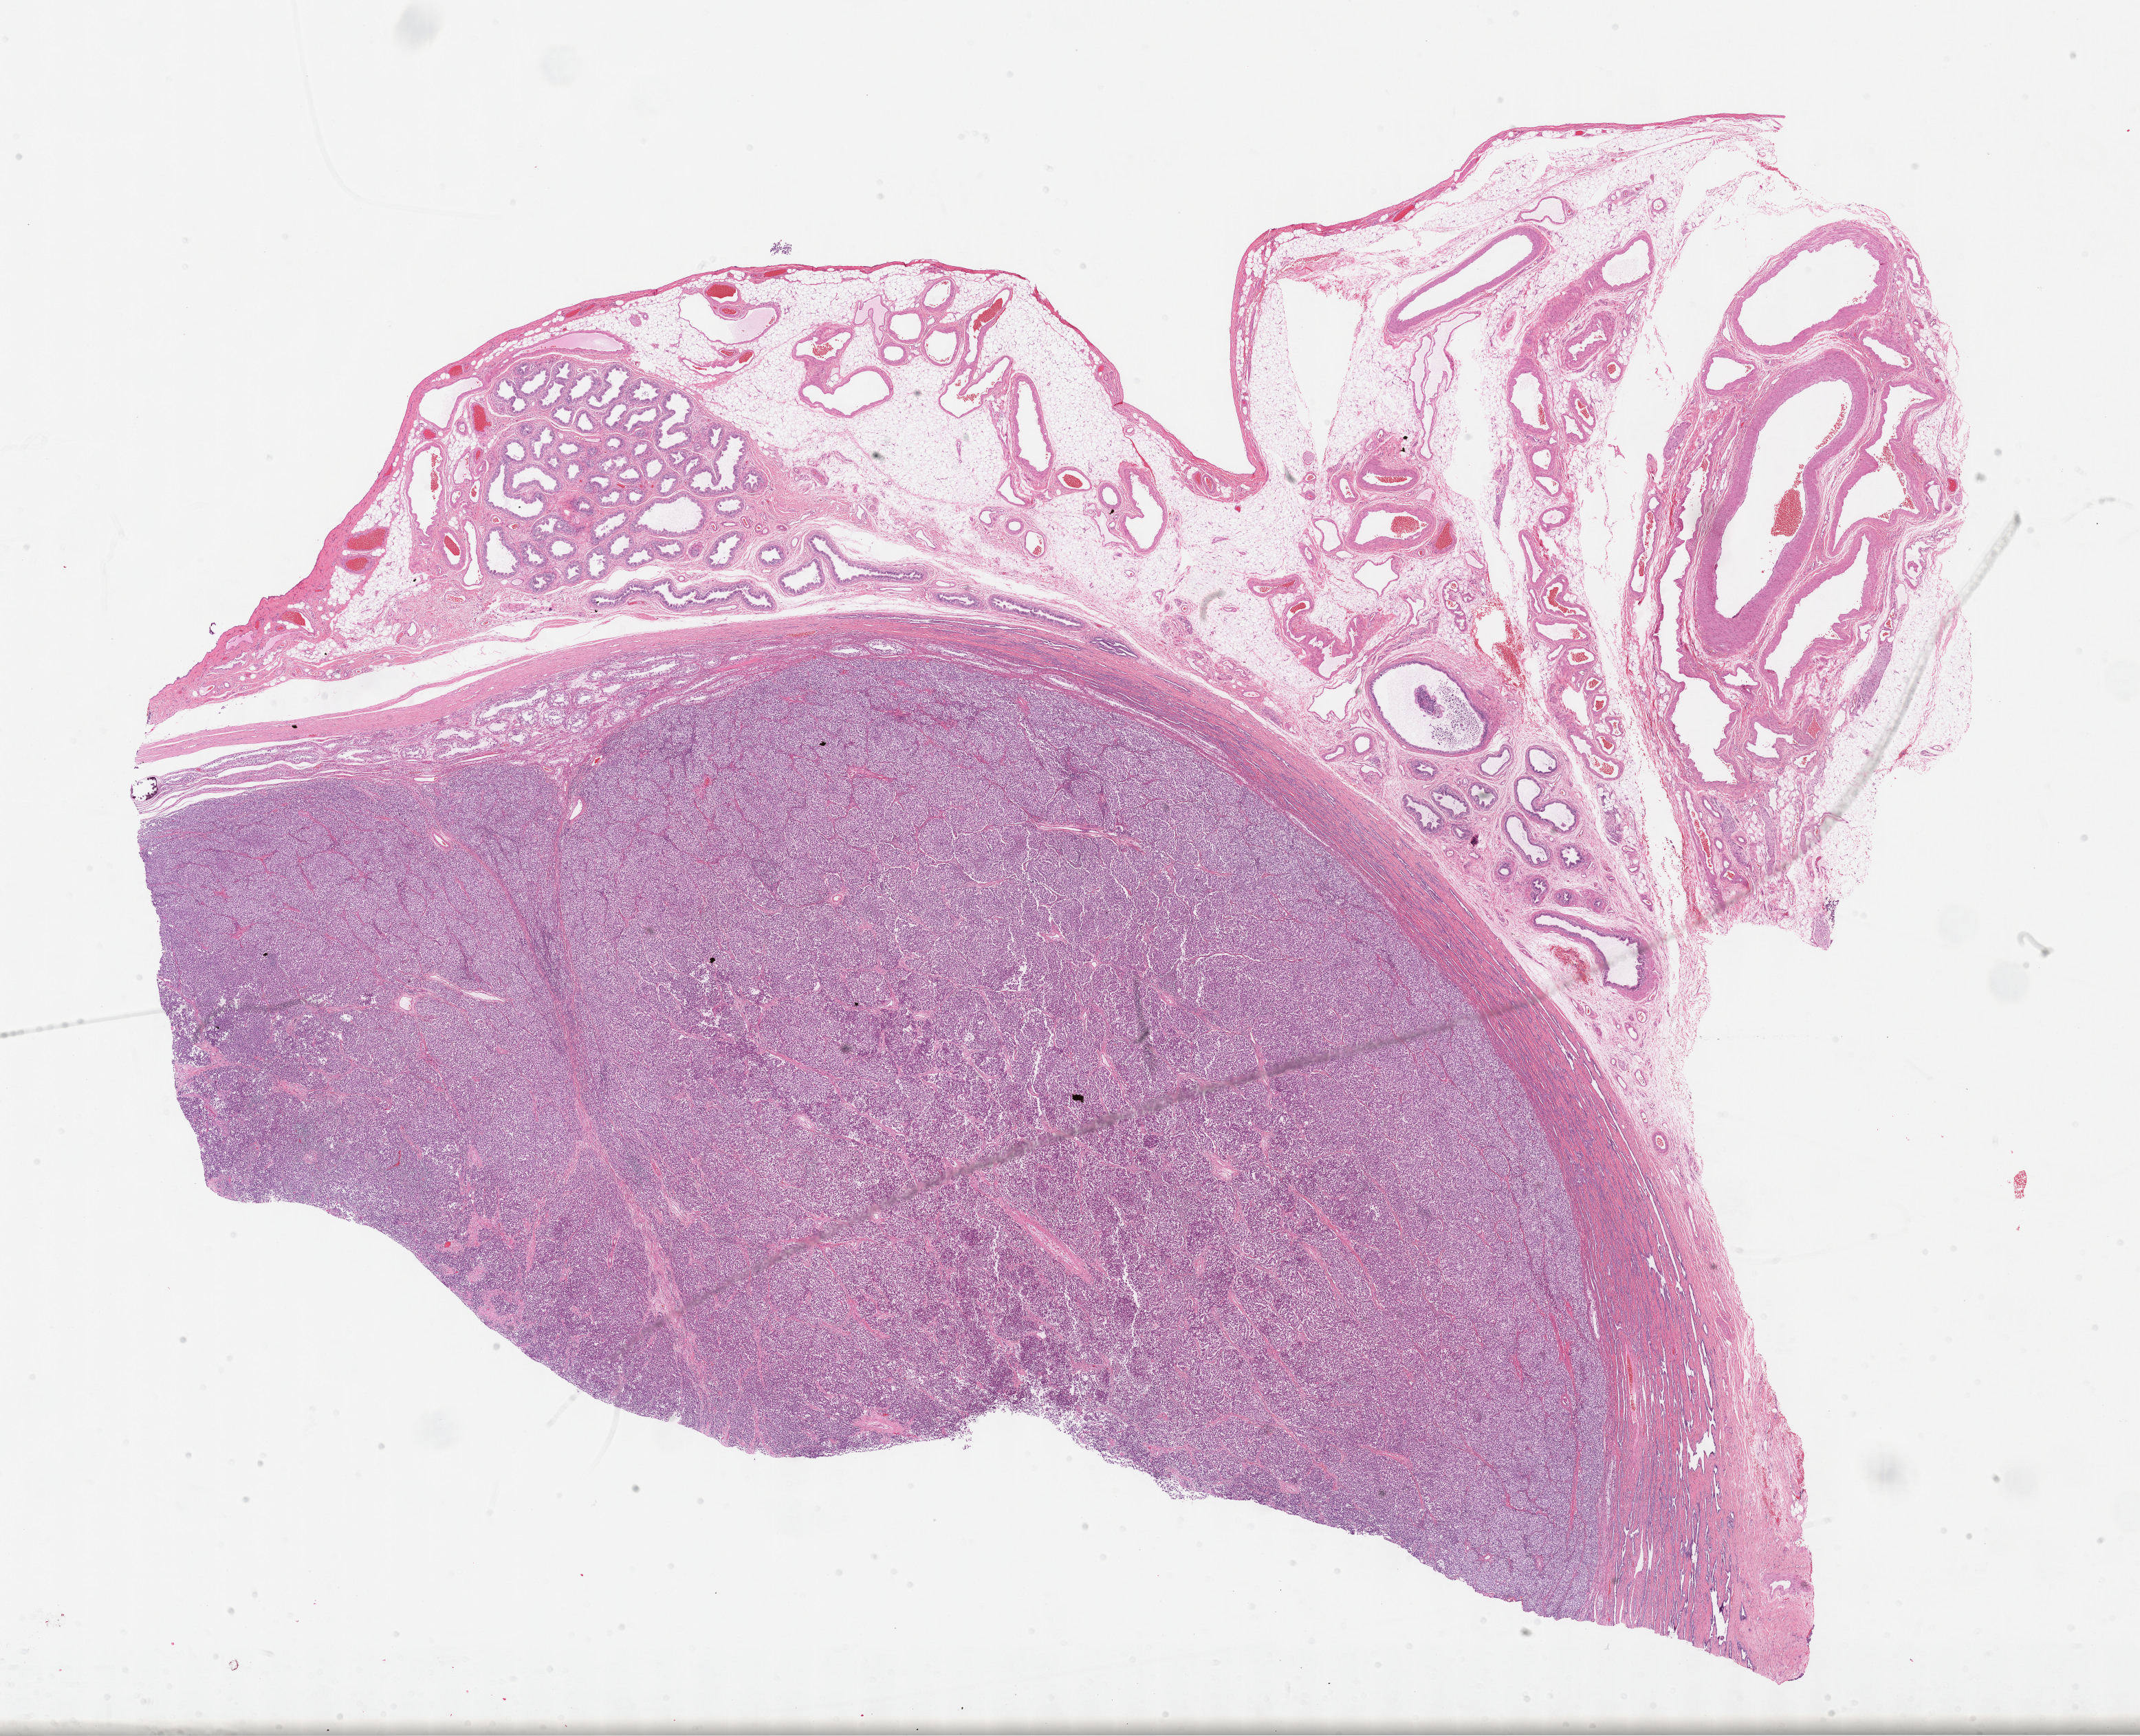
Whole-slide histology image, H&E — a low-resolution overview of the entire scanned area, about 25.2 x 20.4 mm, FFPE section, primary tumour sample from the testis. Patient: male, age at initial diagnosis 38 years.
Diagnosis: Seminoma, NOS.